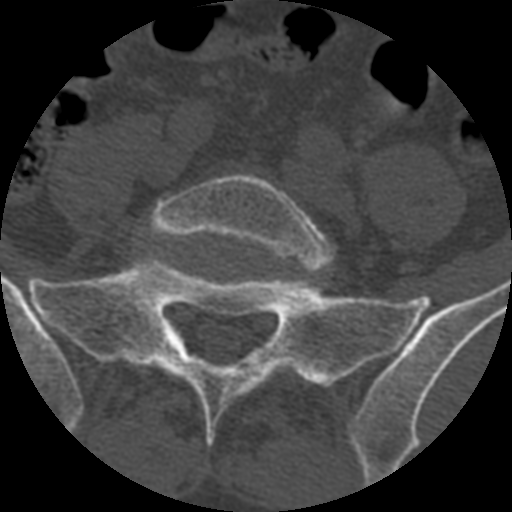
CT including the spine, one axial slice. Reconstruction kernel STANDARD. 120 kVp. Bone window (W 1800 / L 400 HU). 512 × 512 image matrix, field of view 160 × 160 mm. Patient age 71 years. From the clinical record (not read from this slice): primary cancer: prostate.
Structures marked on this image (semi-automatically segmented with operator editing):
- L5 vertebra: bounding box <147,173,335,270> (left, top, right, bottom; pixels)